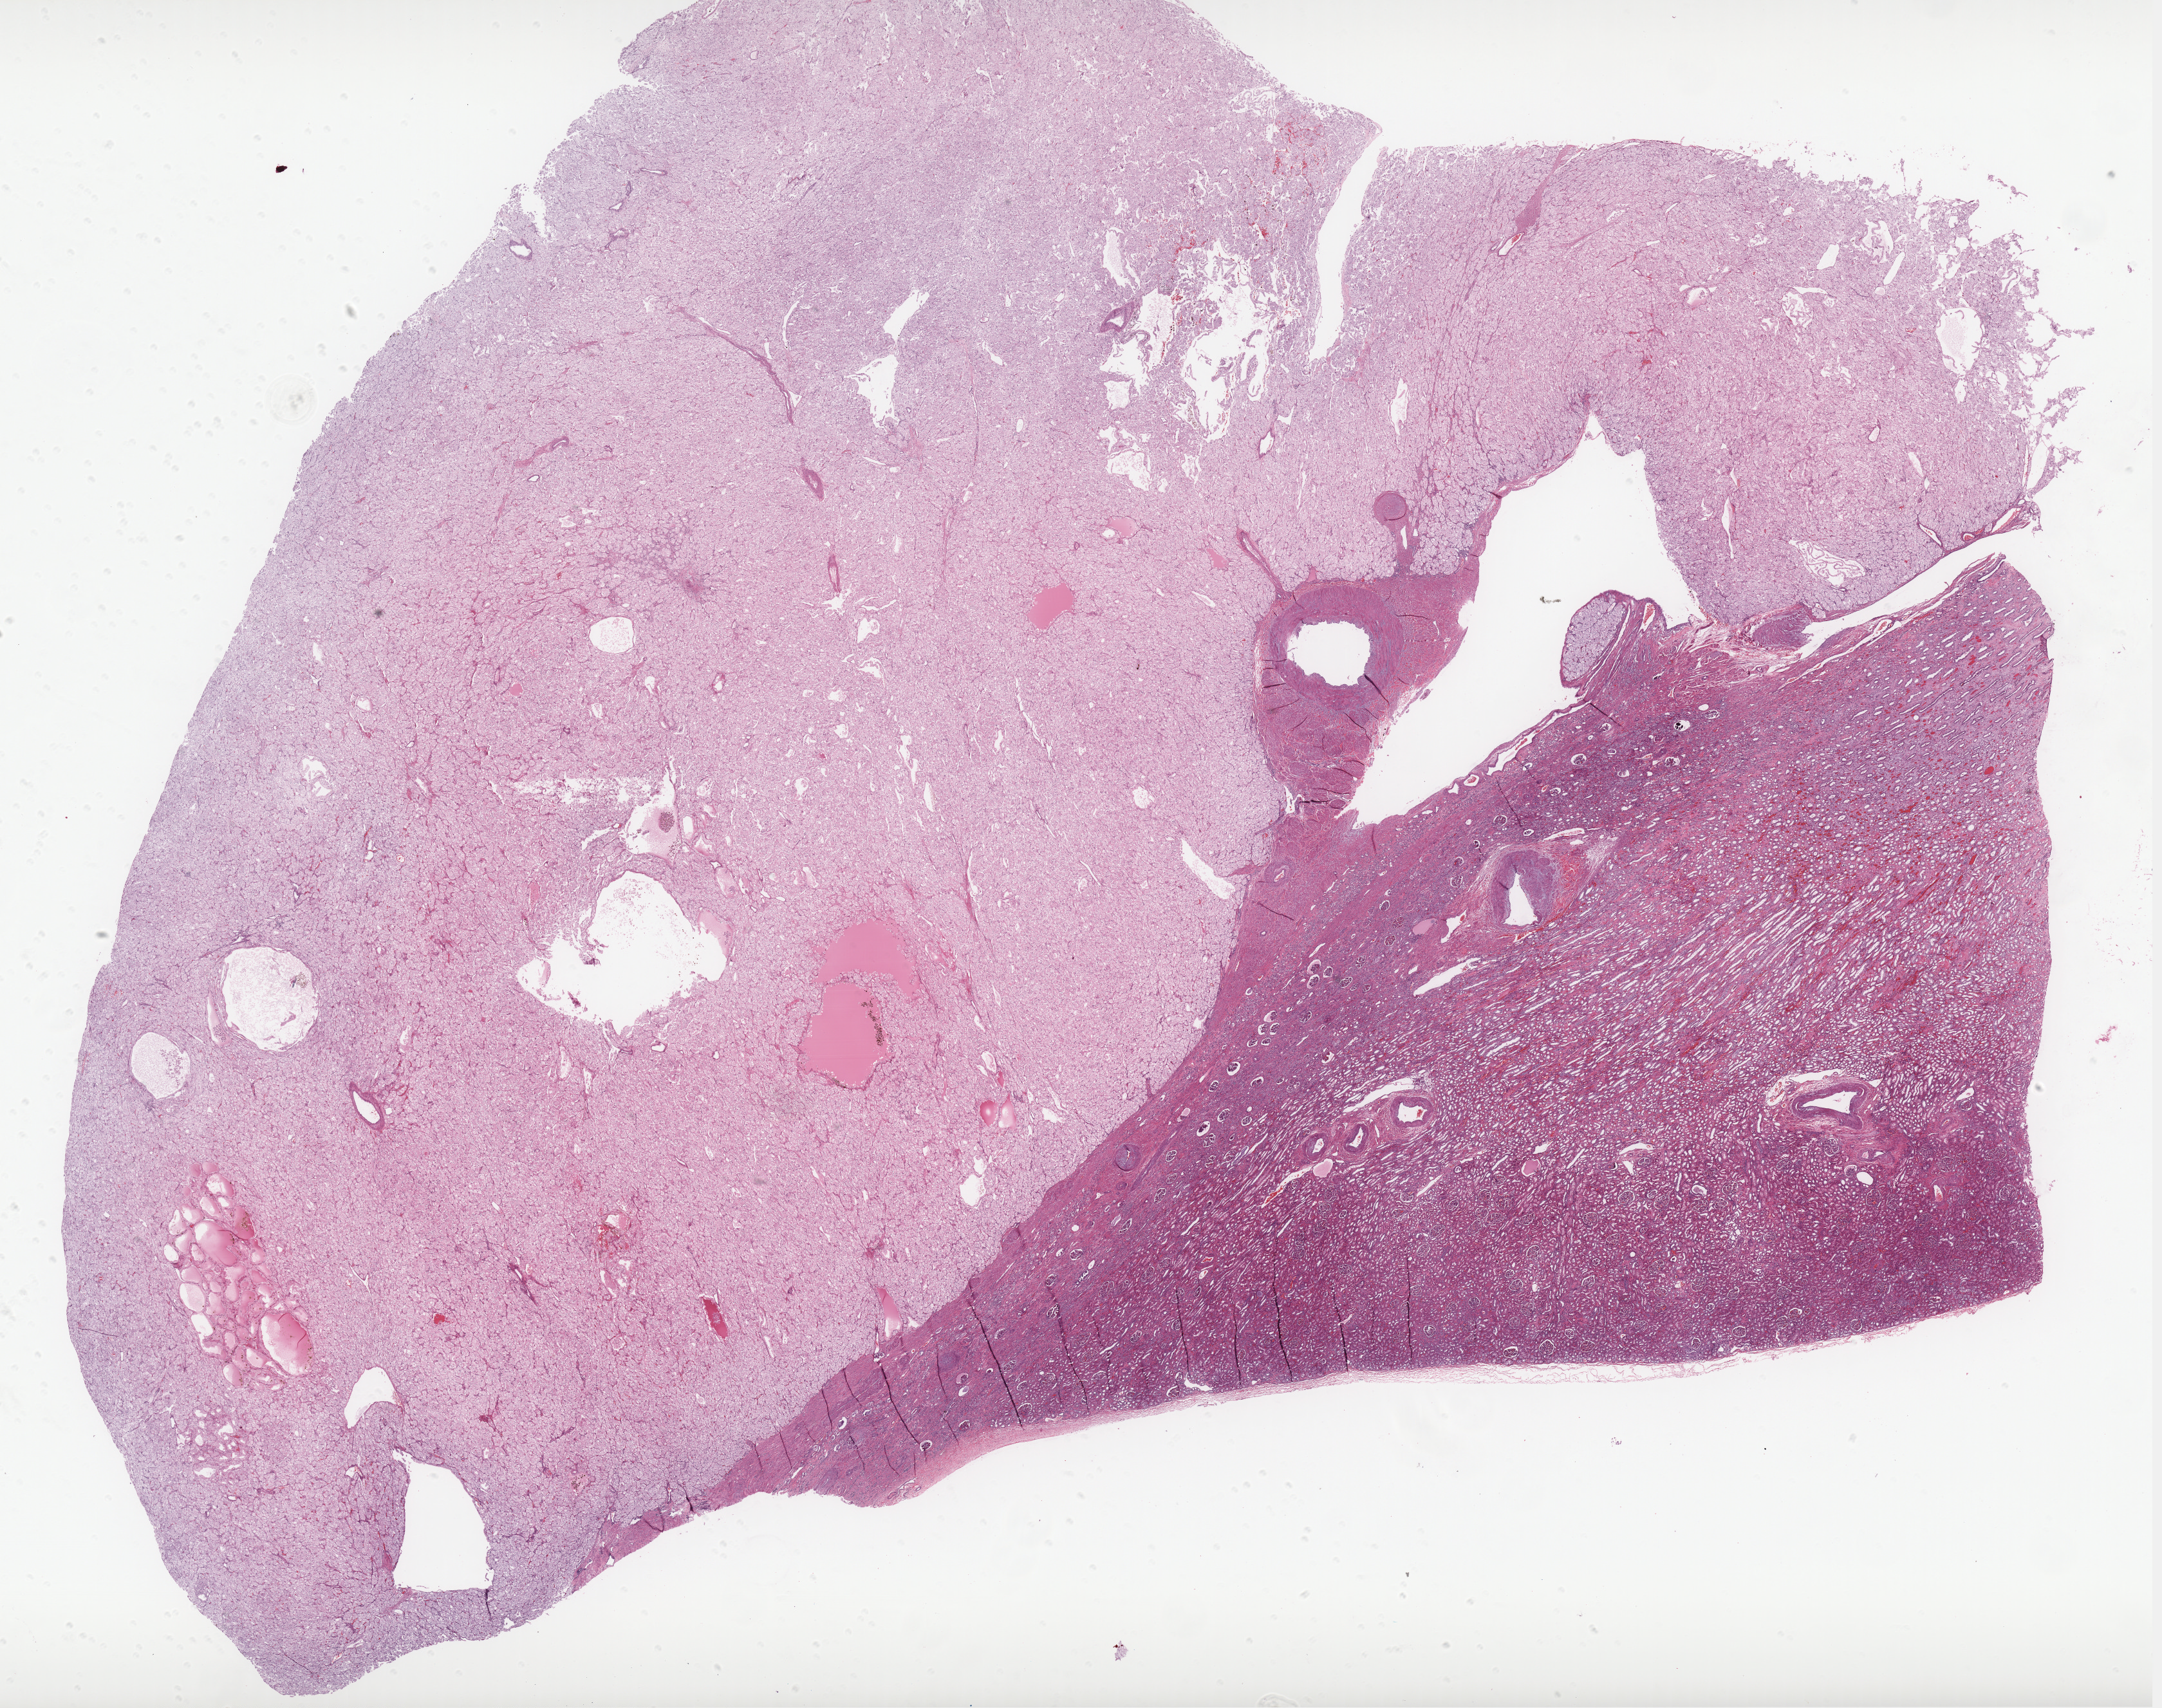
H&E-stained whole-slide image, a low-resolution overview of the entire scanned area, about 26.9 x 21.2 mm; FFPE section; primary tumour sample from the kidney. Male, age 69 years at initial diagnosis.
- laterality: left
- AJCC pathologic stage: II (6th edition)
- lymph nodes positive (case pathology): 0 of 5 examined
- histologic diagnosis: Renal cell carcinoma, chromophobe type